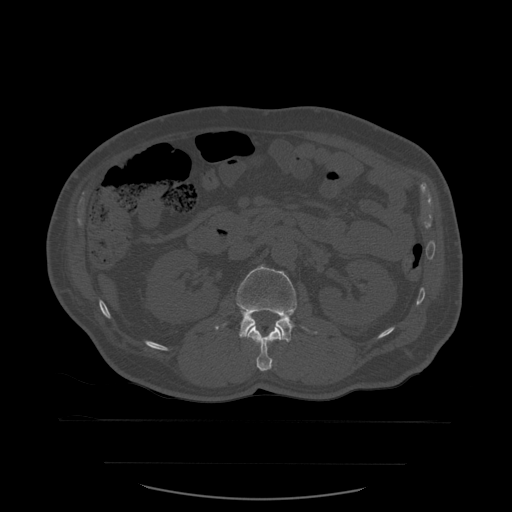
CT including the spine, one axial slice. Position 230 of 590 along the scan axis. Bone window (W 1800 / L 400 HU). 512 × 512 image matrix, field of view 479 × 479 mm. Patient age 71 years. Case-level facts recorded for this patient, not image findings: primary cancer: lung; vertebrae with lytic lesions (as recorded): T1, T2, L5, S1.
Outlined on this slice (semi-automatic segmentation, software-assisted and operator-edited):
- L1 vertebra: bounding box (x1, y1, x2, y2) in pixels: (247, 326, 282, 371)
- L2 vertebra: (215, 265, 318, 343)